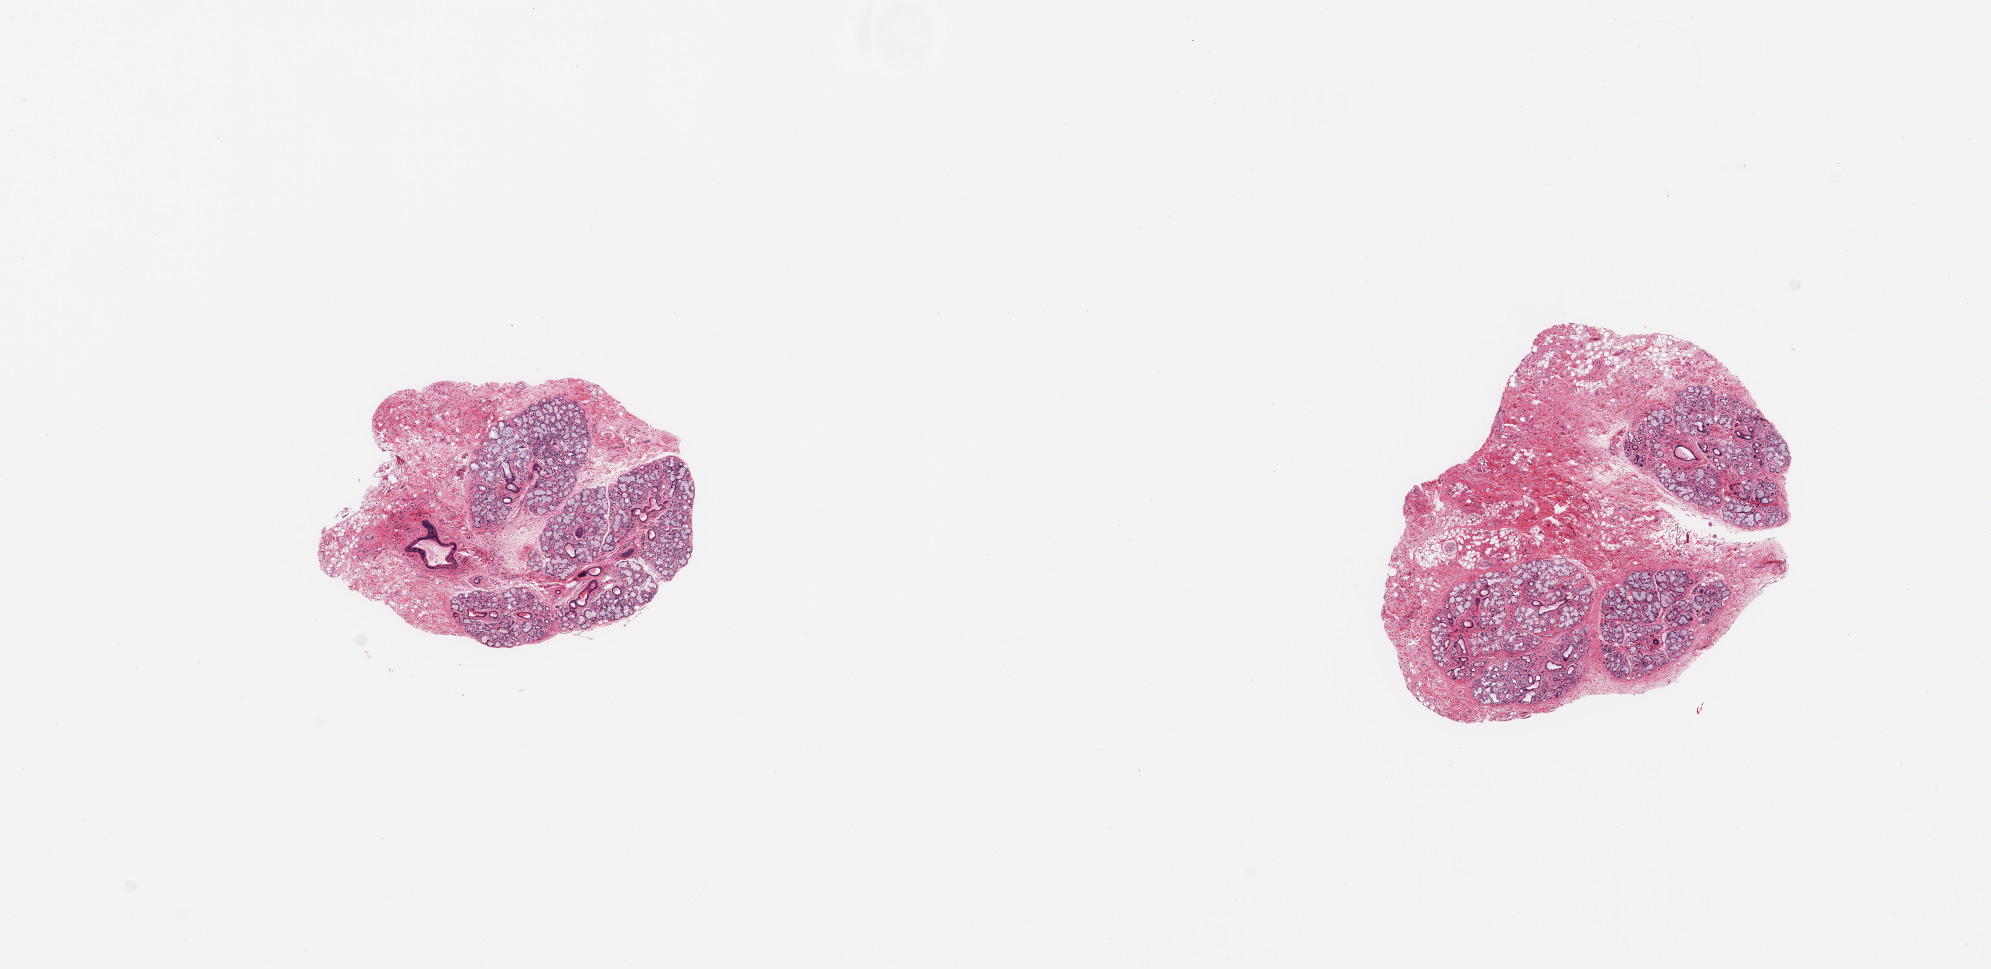
Whole-slide image, haematoxylin and eosin stain — whole scanned area (about 15.8 x 7.7 mm, slide scanned at 20x) shown as a low-resolution overview; PAXgene-fixed paraffin-embedded (PFPE) section; sampled site (target tissue): minor salivary gland; donor tissue sample.
Review note (as recorded): 2 pieces; salivary gland elements embedded in ~40-50% fibrovascular and fatty stroma, focal collection of chronic inflammatory cells.